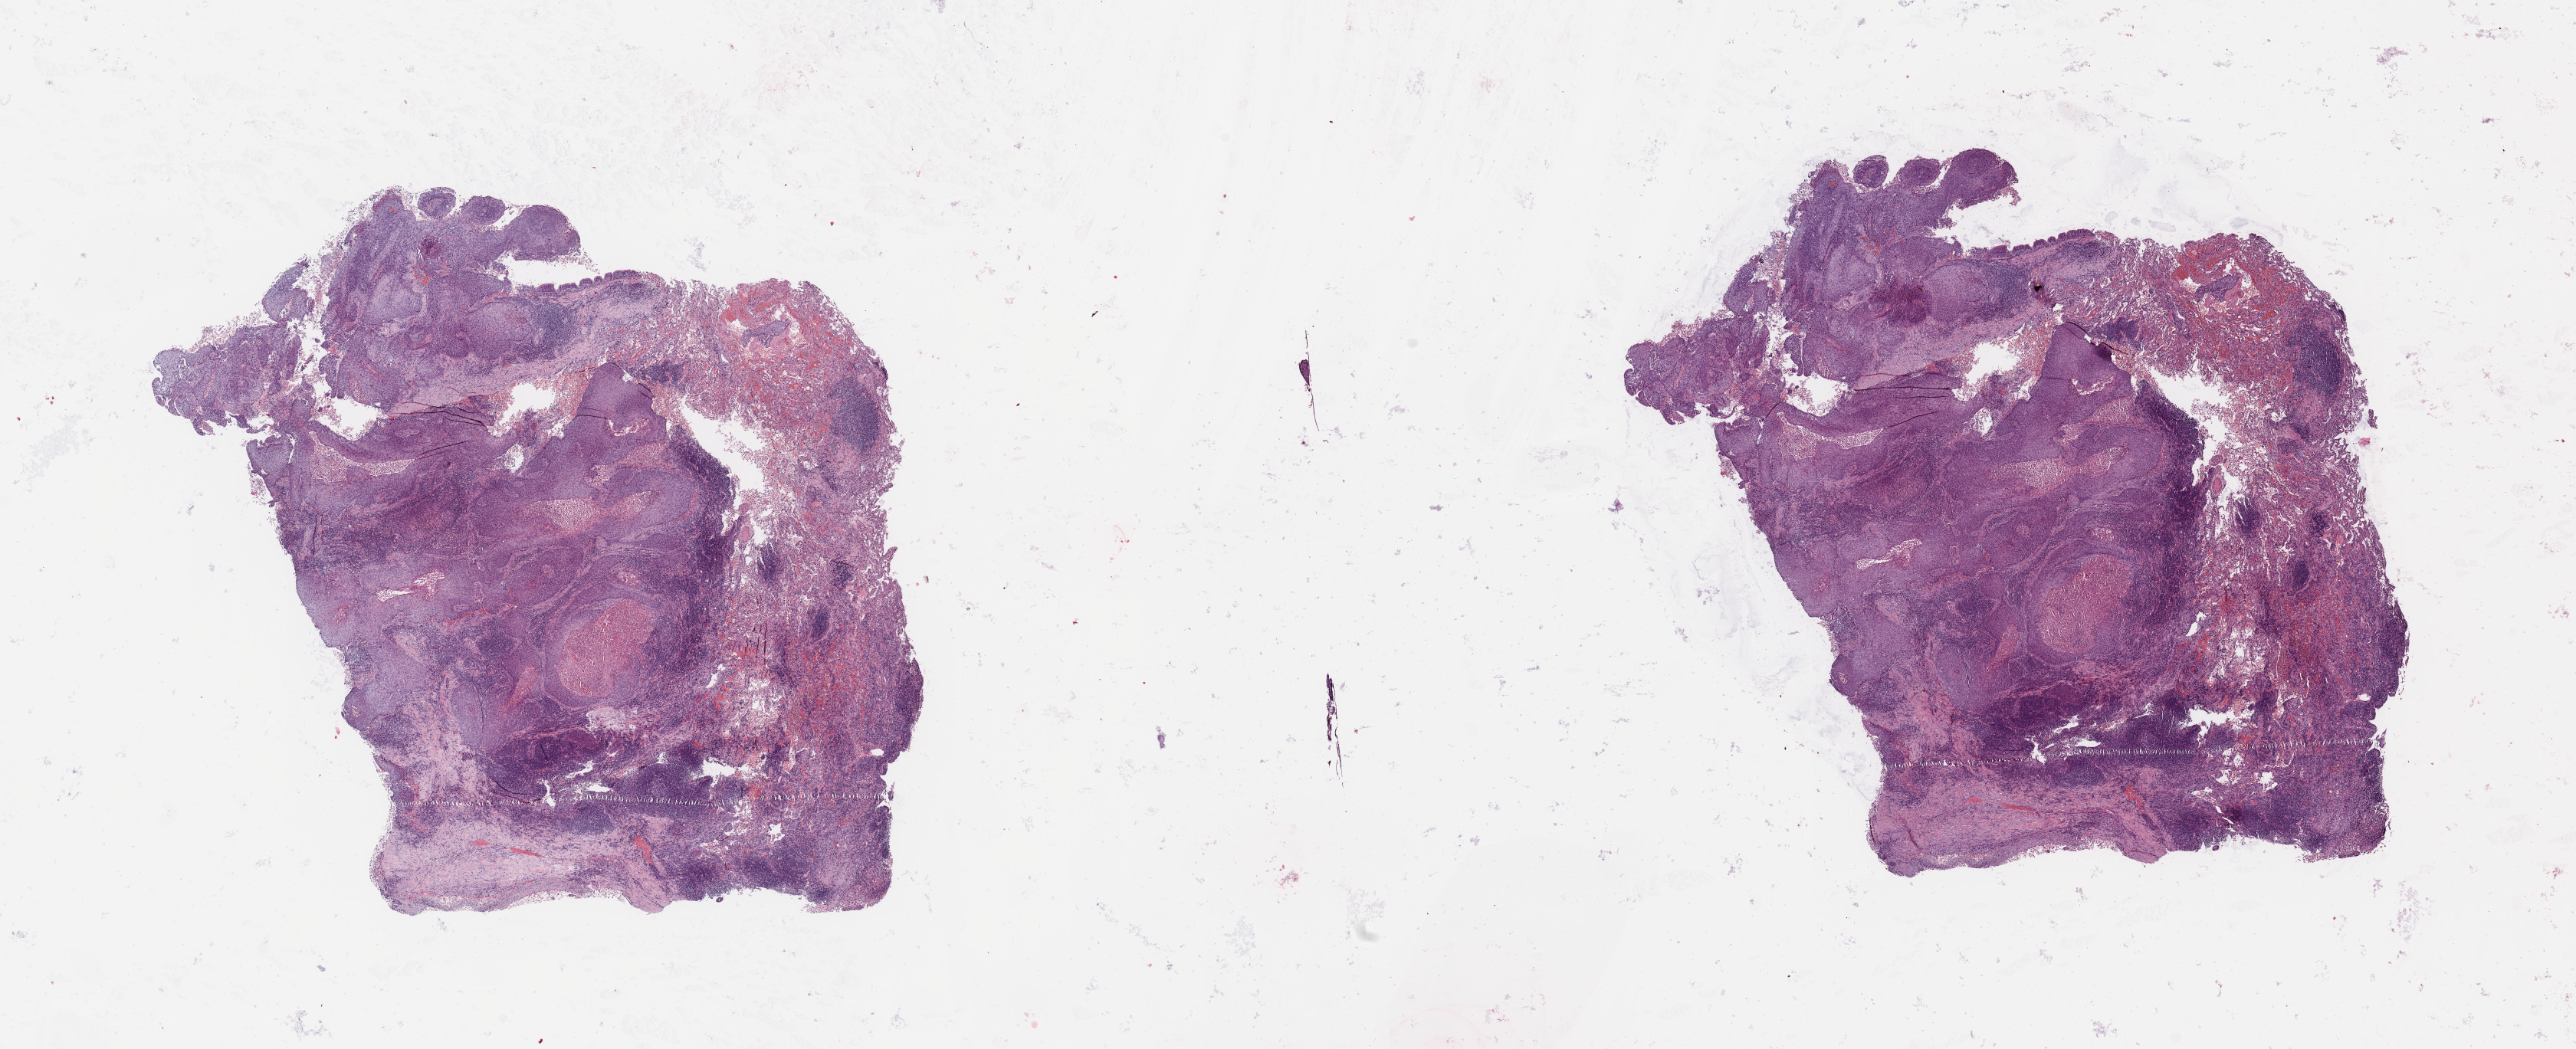
Whole-slide histology image, H&E, shown as a low-resolution overview of the whole scanned area (about 26.6 x 10.8 mm, from a 20x scan). Tumour tissue sample, sampled site: lung. Patient: female, age 48 years. Histologic grade: G2 (moderately differentiated). Slide review estimates, as recorded: tumour nuclei 65%, necrosis 10%.
• AJCC pathologic stage: IB
• histologic diagnosis: Squamous cell carcinoma, NOS
• primary tumour site (as recorded): left upper lobe